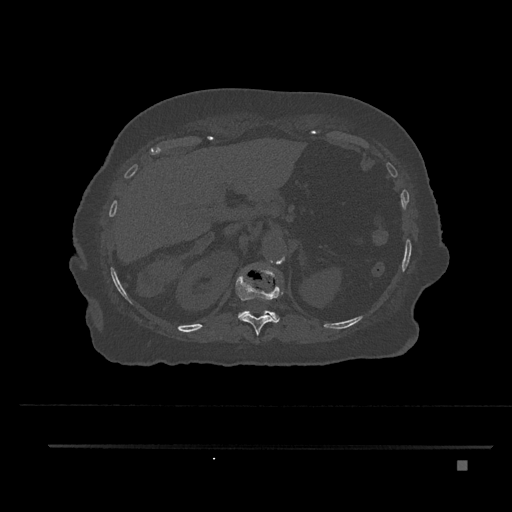
CT including the spine, one axial slice. Slice 298 of 797 in the series (ordered by position). Reconstruction kernel Br40s/3. Bone window (W 1800 / L 400 HU). 0.5 mm slice thickness. 512 × 512 image matrix, field of view 437 × 437 mm. Female patient, age 76 years. Case-level facts recorded for this patient, not image findings: primary cancer: lung; vertebrae with lytic lesions (as recorded): T11, L3.
Annotated regions visible in this slice (semi-automatic segmentation, software-assisted and operator-edited):
- T11 vertebra: bounding box <235,273,283,336> (left, top, right, bottom; pixels)
- T12 vertebra: <238,282,280,322>